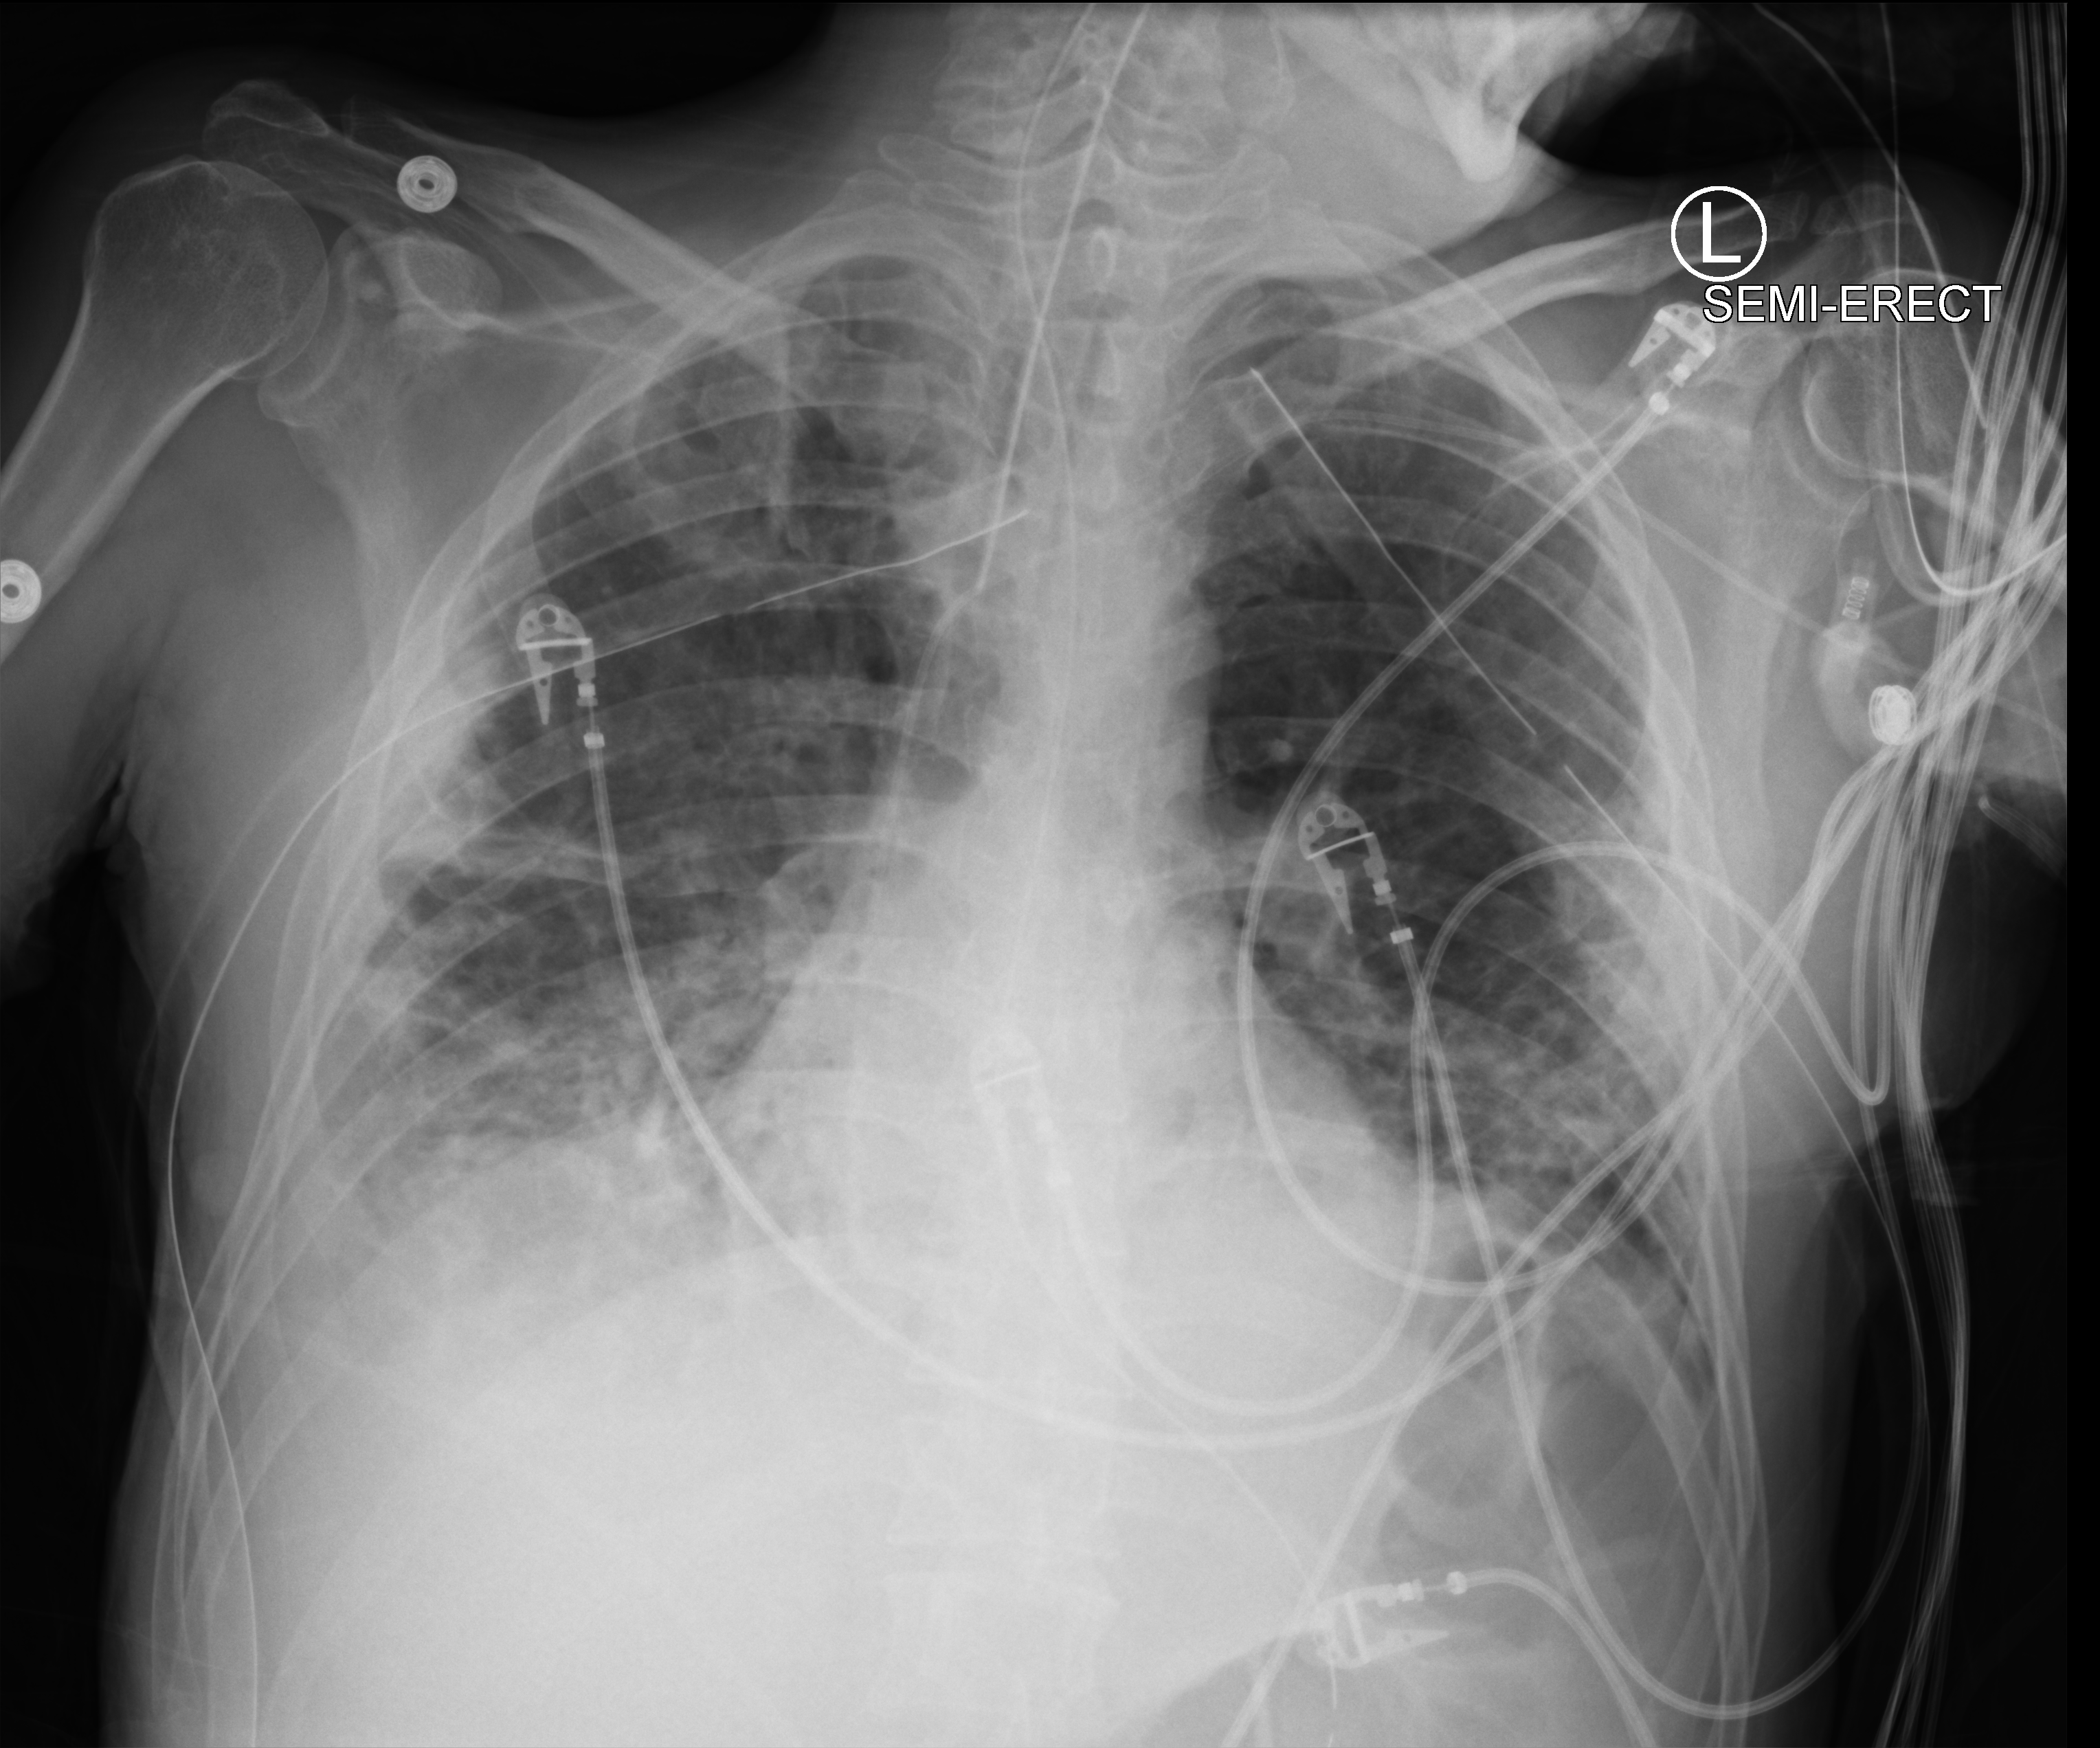
Chest X-ray (portable), anteroposterior (AP) projection. Patient hospitalised with COVID-19; male, aged 18–59 years.
Admission-level facts for this patient (not findings on this image; timing relative to this image not recorded): other chronic lung disease (admission record): no; admitted to intensive care during this hospital stay: yes.